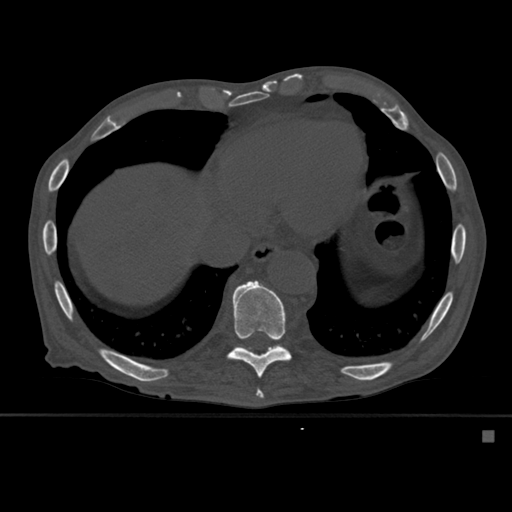
CT including the spine, one axial slice. Slice 314 of 527 in the series (ordered by position). Bone window (W 1800 / L 400 HU). 512 × 512 image matrix. Male patient, age 78 years. Case-level facts recorded for this patient, not image findings: primary cancer: prostate.
Outlined on this slice (semi-automatic segmentation, software-assisted and operator-edited):
- T10 vertebra: bounding box [x1, y1, x2, y2] px = [226, 280, 292, 378]
- T11 vertebra: [240, 340, 284, 350]
- T9 vertebra: [256, 389, 264, 399]